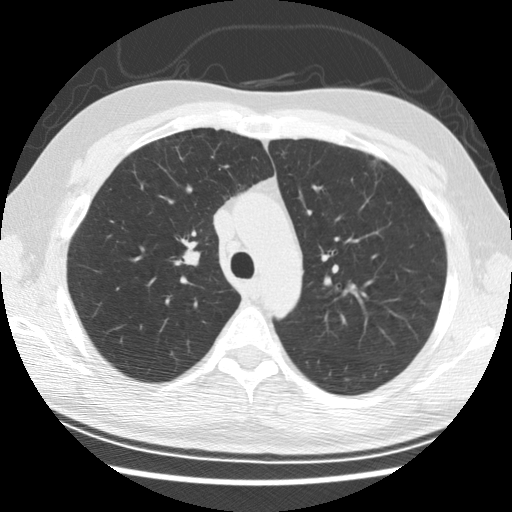
Low-dose screening chest CT, axial slice. Baseline annual screen. Lung window (W 1500 / L -600 HU). 2.5 mm slice thickness. Standard (soft-tissue) reconstruction kernel (STANDARD). 120 kVp. Slice 83 of 278 in the series. Male participant, aged 57 years at enrolment. Former smoker at enrolment.
Expert-annotated lung lesion, box from (x=163, y=221) to (x=220, y=282) px. The screening reader recorded 6 non-calcified nodules or masses ≥4 mm on this exam (right middle lobe, right middle lobe, right lower lobe, right middle lobe, right middle lobe, right lower lobe); which of them this box marks is not recorded. Later outcome: lung cancer diagnosed 766 days after this screen — adenocarcinoma, NOS, right upper lobe, poorly differentiated (G3), stage IB (AJCC 6th edition), 25 mm at pathology.